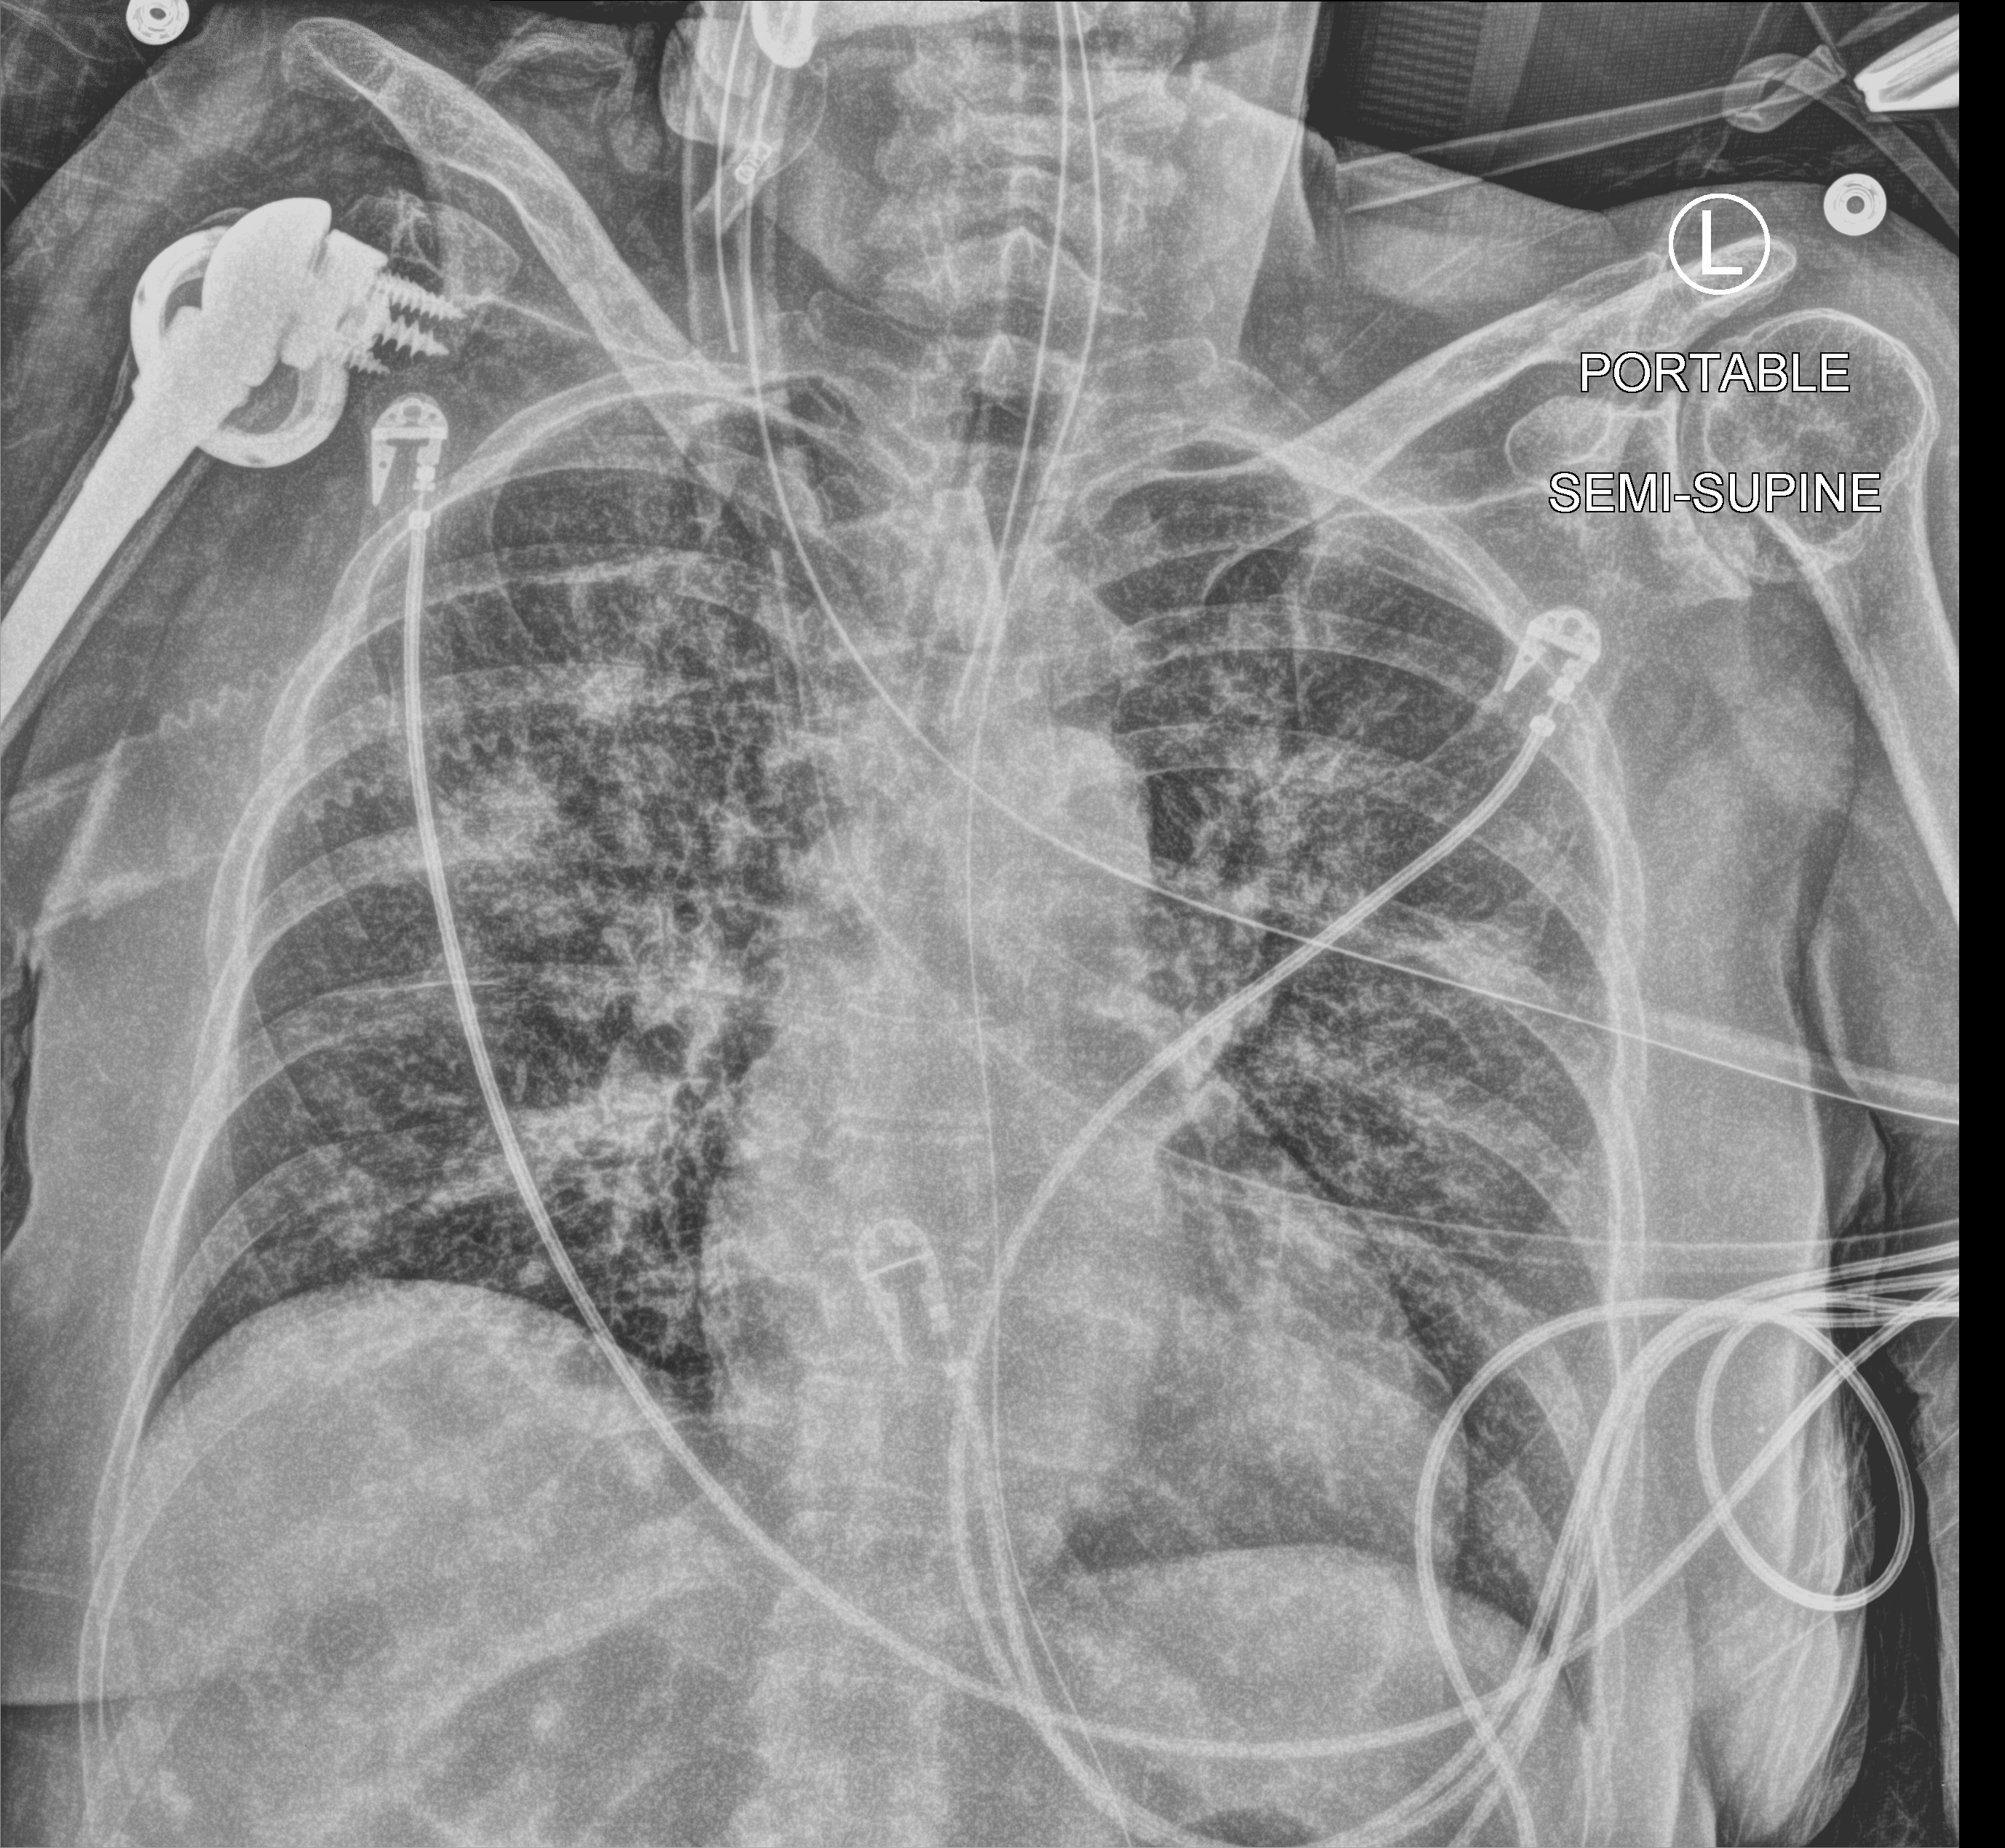
Chest X-ray (portable), anteroposterior (AP) projection. Female patient hospitalised with COVID-19, age 60–74 years.
Admission-level facts for this patient (not findings on this image; timing relative to this image not recorded):
- admitted to intensive care during this hospital stay: yes
- mechanically ventilated during this hospital stay: yes